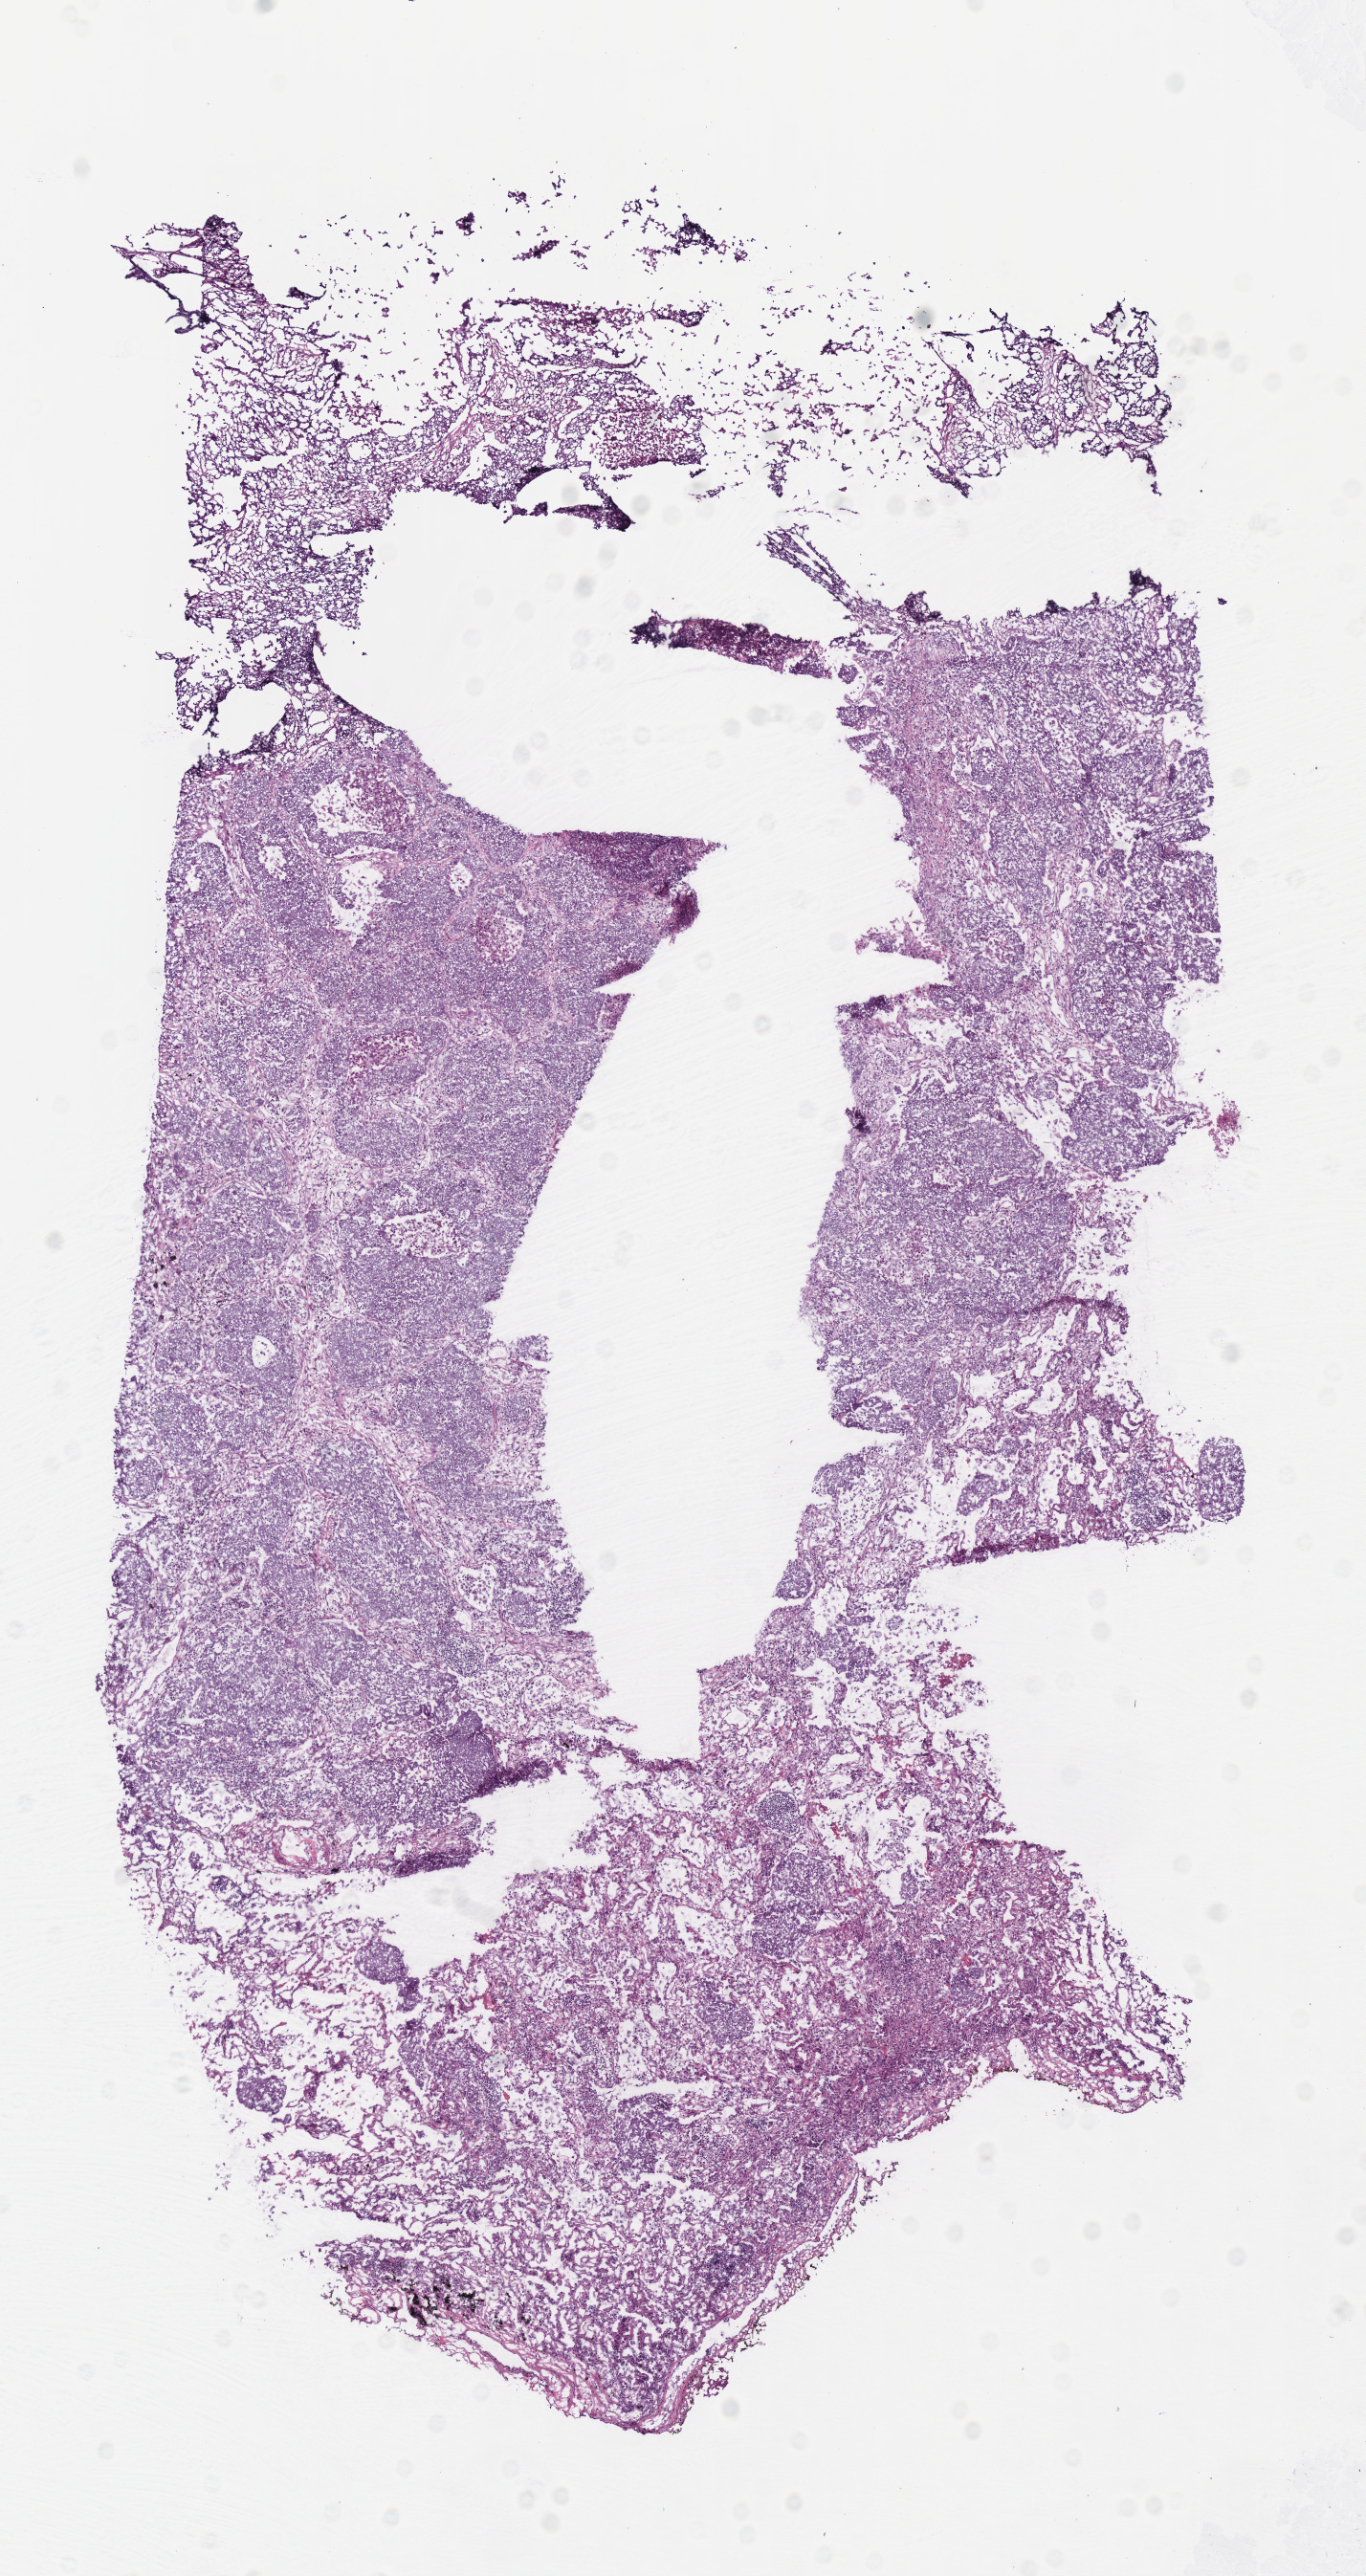
Whole-slide histology image, H&E — low-resolution overview of the scanned area, about 5.6 x 10.6 mm (acquisition: 40x scan), frozen section from the bottom of the tissue portion, primary tumour sample from the lung. Patient: male, age at initial diagnosis 68 years. Composition of this section per pathologist review: tumour cells 85%, tumour nuclei 70%, normal cells 15%, stromal cells 0%, necrosis 0%. Inflammatory infiltration, as recorded: lymphocyte infiltration 12%, monocyte infiltration 12%, neutrophil infiltration 4%.
Histologic diagnosis: Squamous cell carcinoma, NOS. Laterality: left.